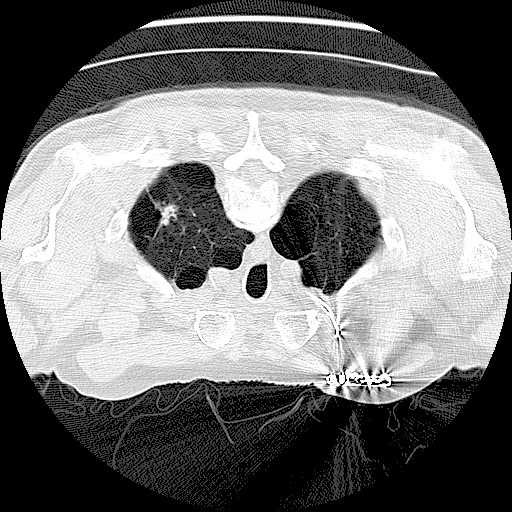
Low-dose screening chest CT, one axial slice. Slice 119 of 138 in the series (ordered by position). Reconstruction kernel LUNG. 120 kVp. Lung window (W 1500 / L -600 HU). 512 × 512 image matrix, field of view 330 × 330 mm.
Annotated regions visible in this slice (expert manual segmentation):
- lesion 1 (tumor): bounding box [x1, y1, x2, y2] px = [158, 203, 178, 229]